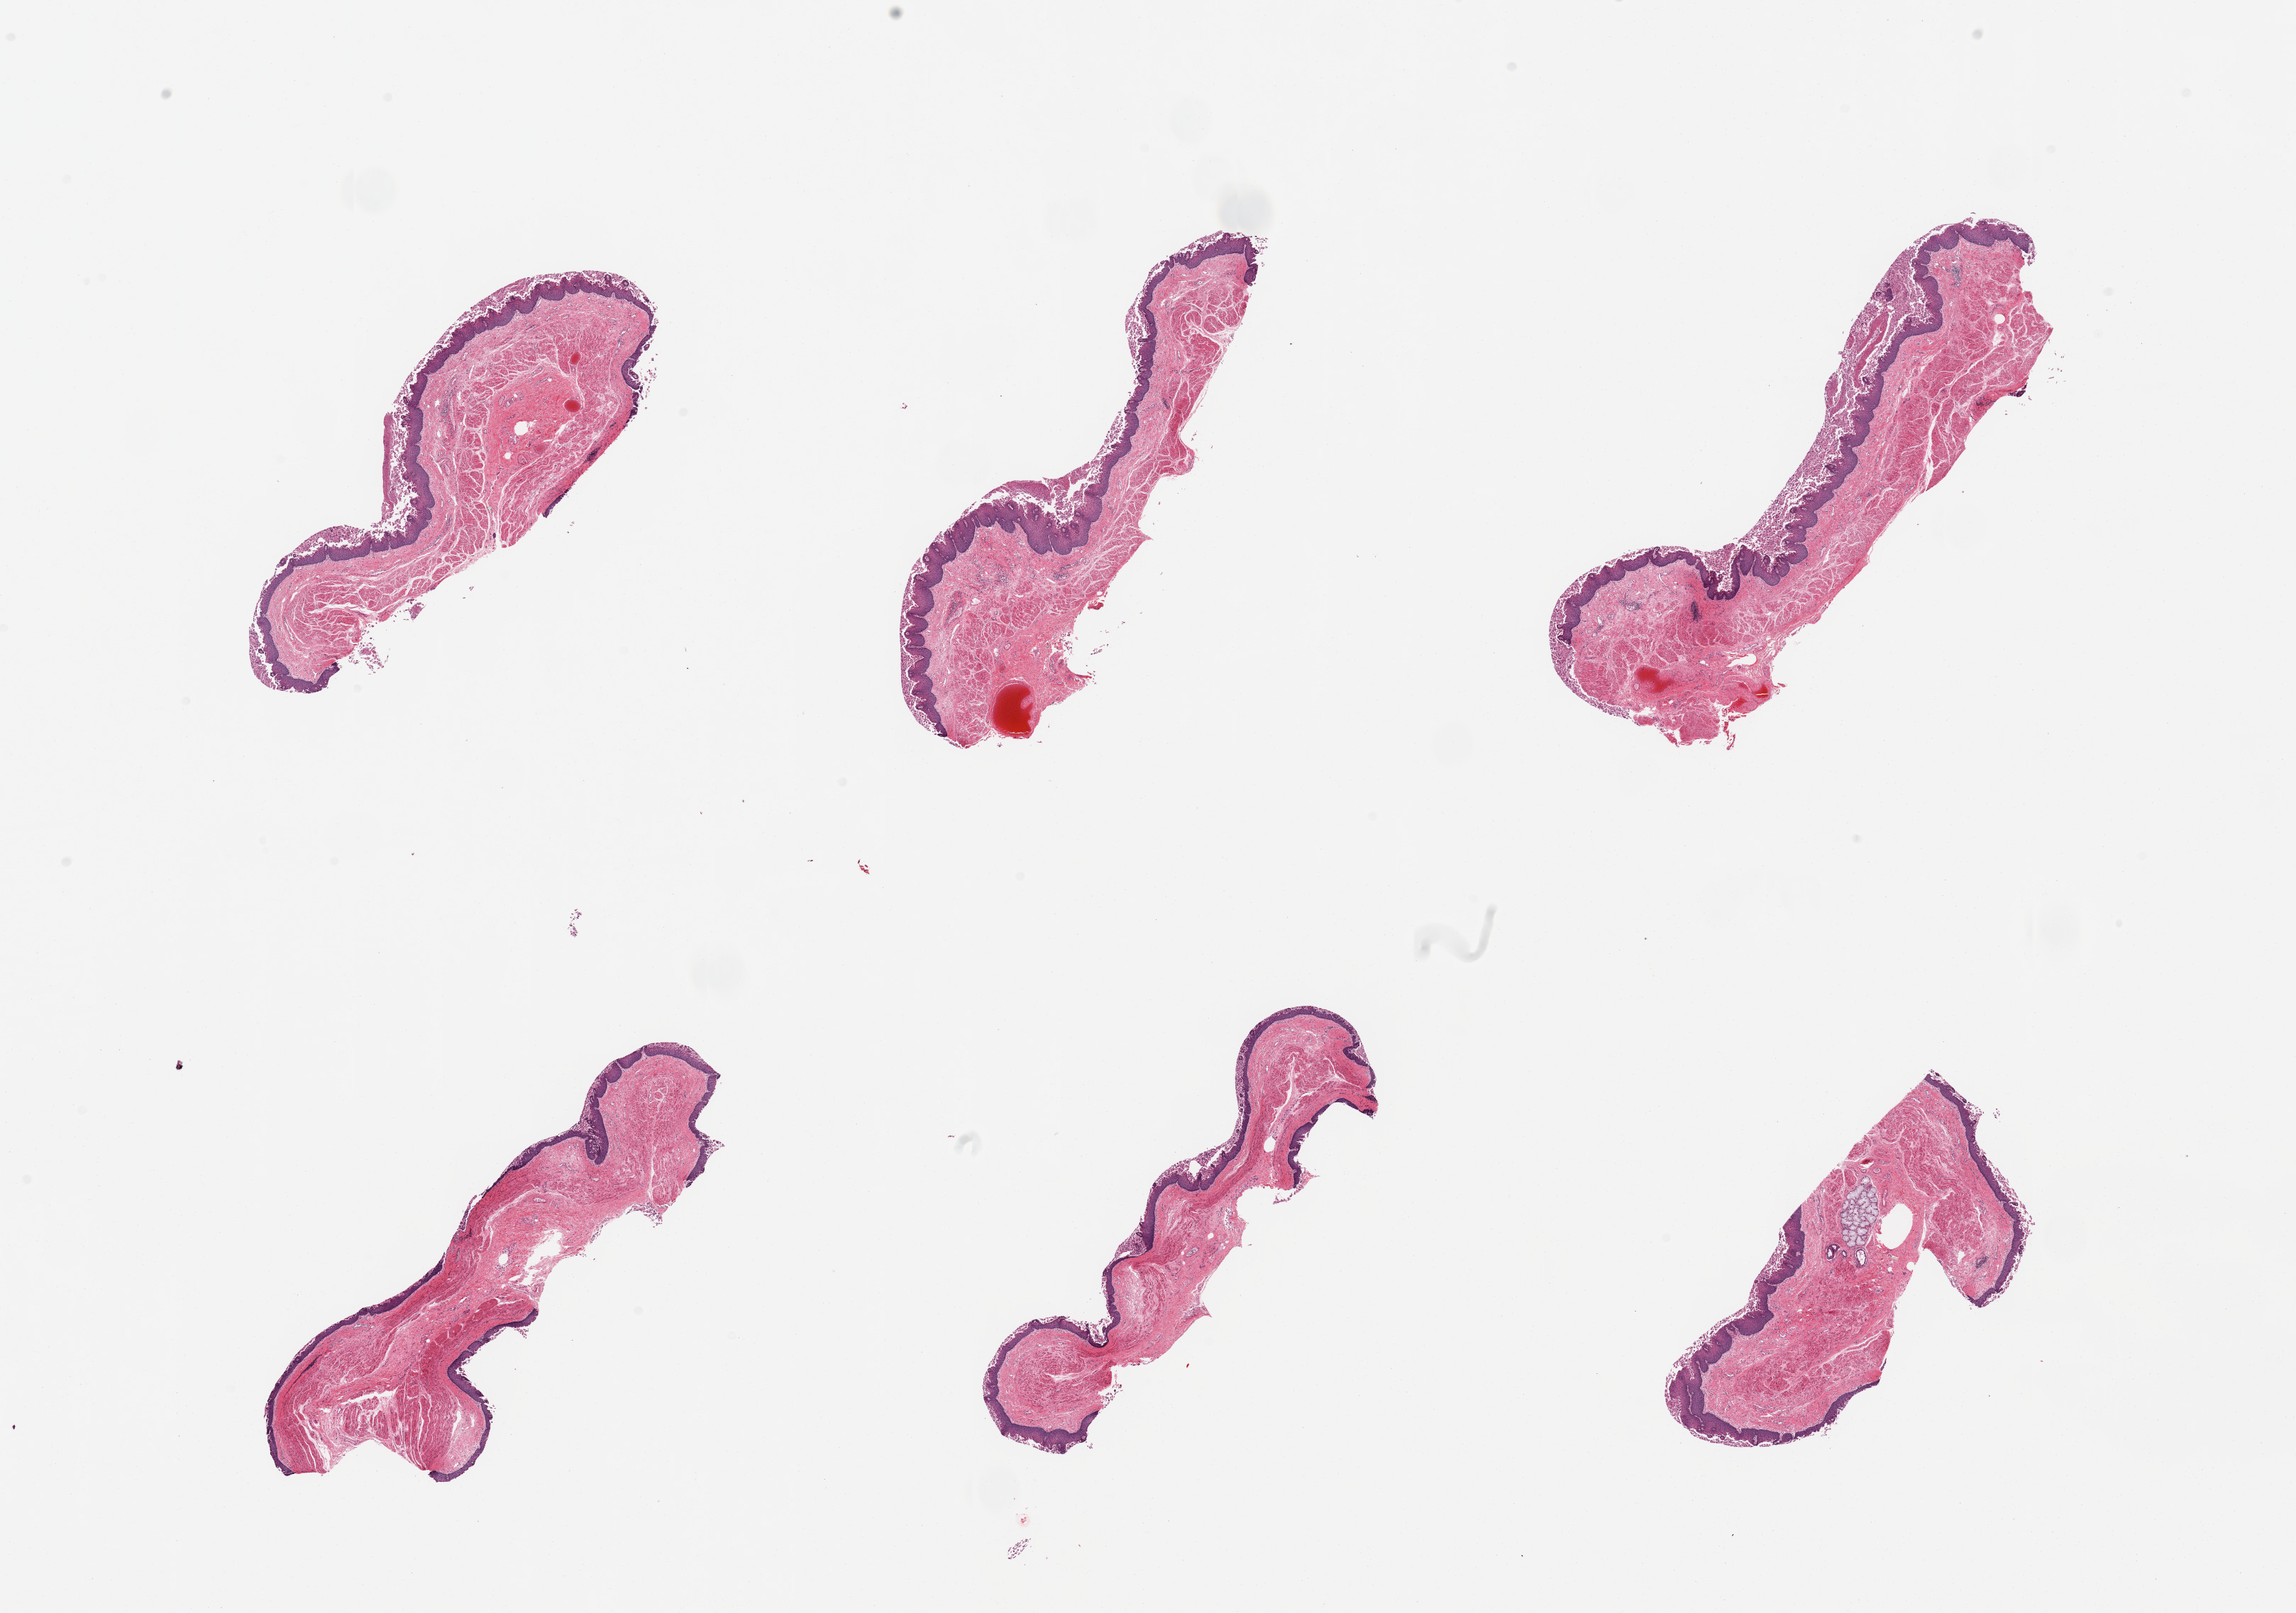
Haematoxylin and eosin whole-slide image, shown as a low-resolution overview of the whole scanned area (about 25.6 x 18.0 mm, acquisition: 20x scan). PAXgene-fixed, paraffin-embedded tissue. Section of esophageal mucous membrane (target tissue). Donor tissue sample. Donor sex: male.
• pathologist's review note for this sample: 6 pieces; sloughing of superficial epithelium, rare submucosal glands